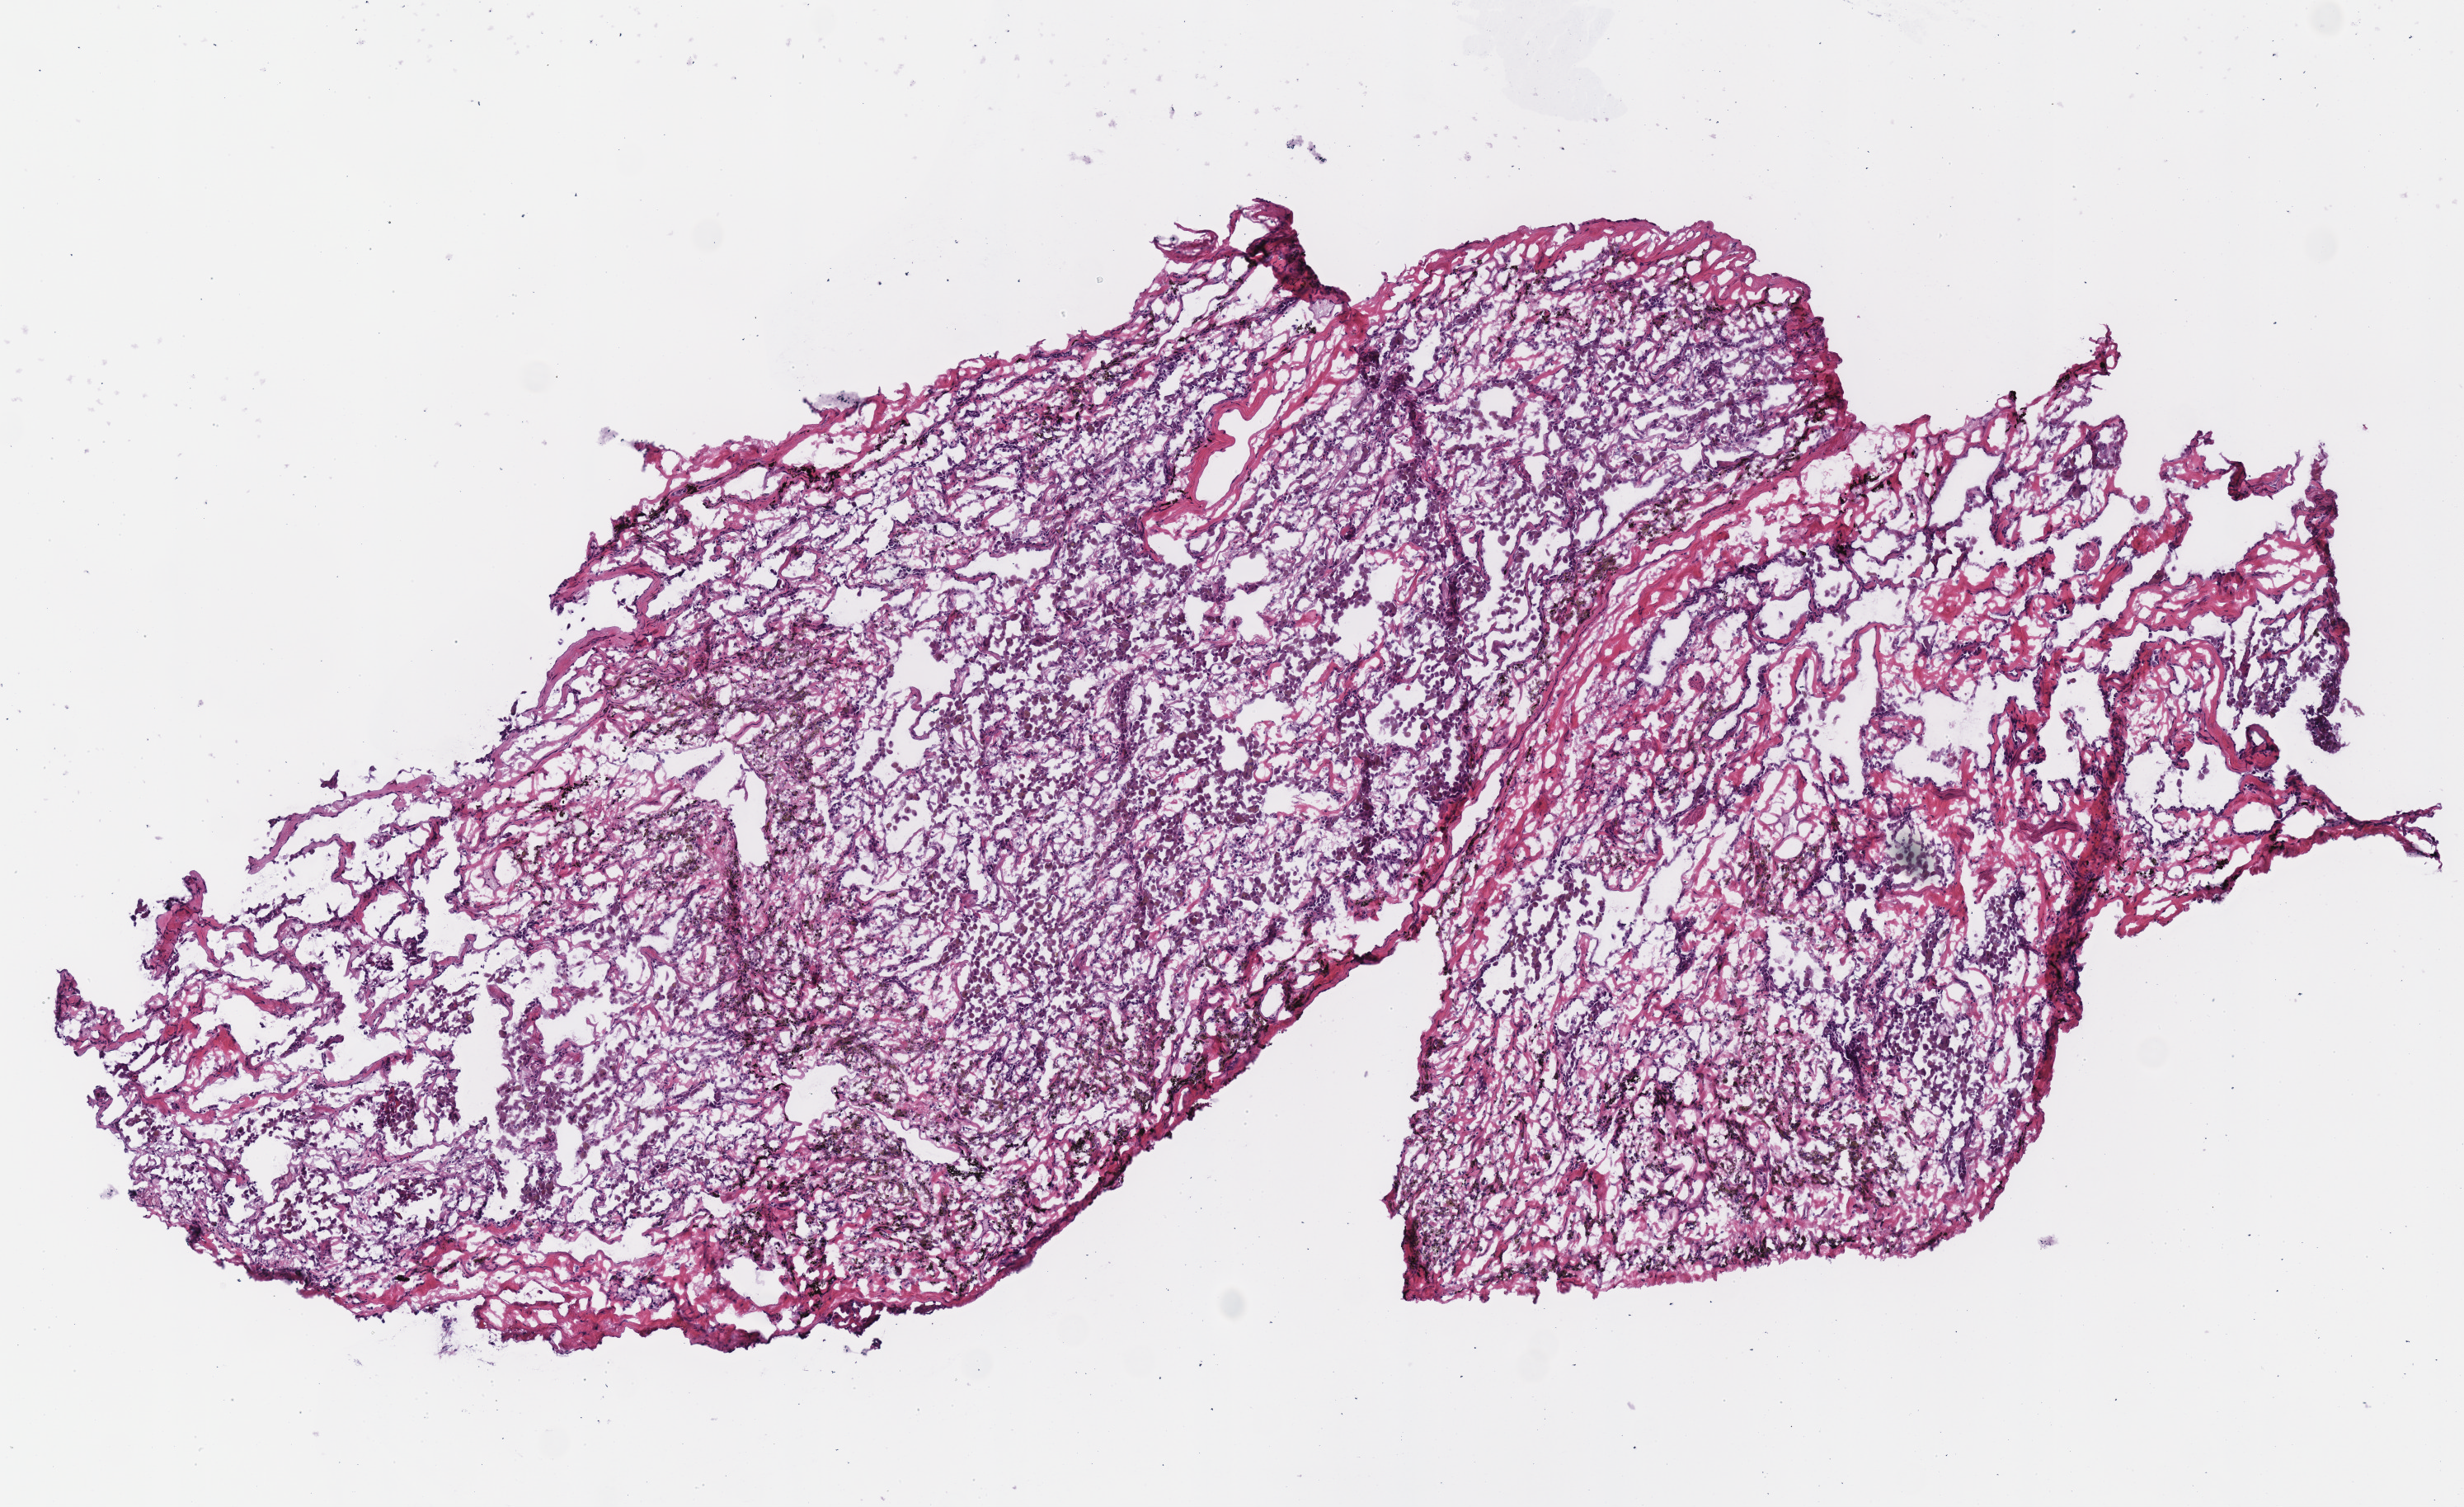
Whole-slide histology image, H&E — whole scanned area (about 5.9 x 3.6 mm, from a 40x scan) shown as a low-resolution overview; frozen section from the top of the tissue portion; lung, solid tissue normal (non-tumour tissue) sample. Male, age 53 years at initial diagnosis.
- this section: solid tissue normal (non-tumour) sample from the same patient
- patient diagnosis: Adenocarcinoma, NOS (upper lobe, lung)